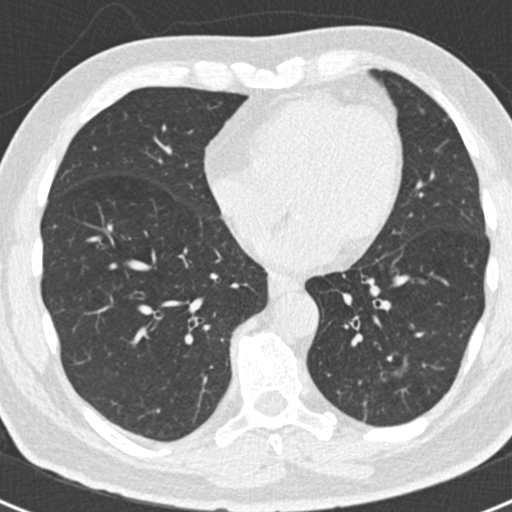
Low-dose screening chest CT, axial slice, baseline screening round, lung window (W 1500 / L -600 HU), 2 mm slice thickness, standard (soft-tissue) reconstruction kernel (B30f), slice 106 of 188 in the series, 512 × 512 image matrix. Male participant, aged 66 years at enrolment. Former smoker at enrolment.
- Lesion marked by an expert reader, bounding box [x1, y1, x2, y2] px = [341, 336, 420, 414].
- Reader record for this screening exam (exam-level; its link to the box is not recorded): non-calcified nodule or mass ≥4 mm, left lower lobe, 43 × 27 mm, smooth margins.
- Participant outcome: lung cancer diagnosed 801 days after this screen (after the third annual screen) — adenocarcinoma, NOS, left lower lobe, poorly differentiated (G3), stage IB (AJCC 6th edition), 38 mm at pathology.